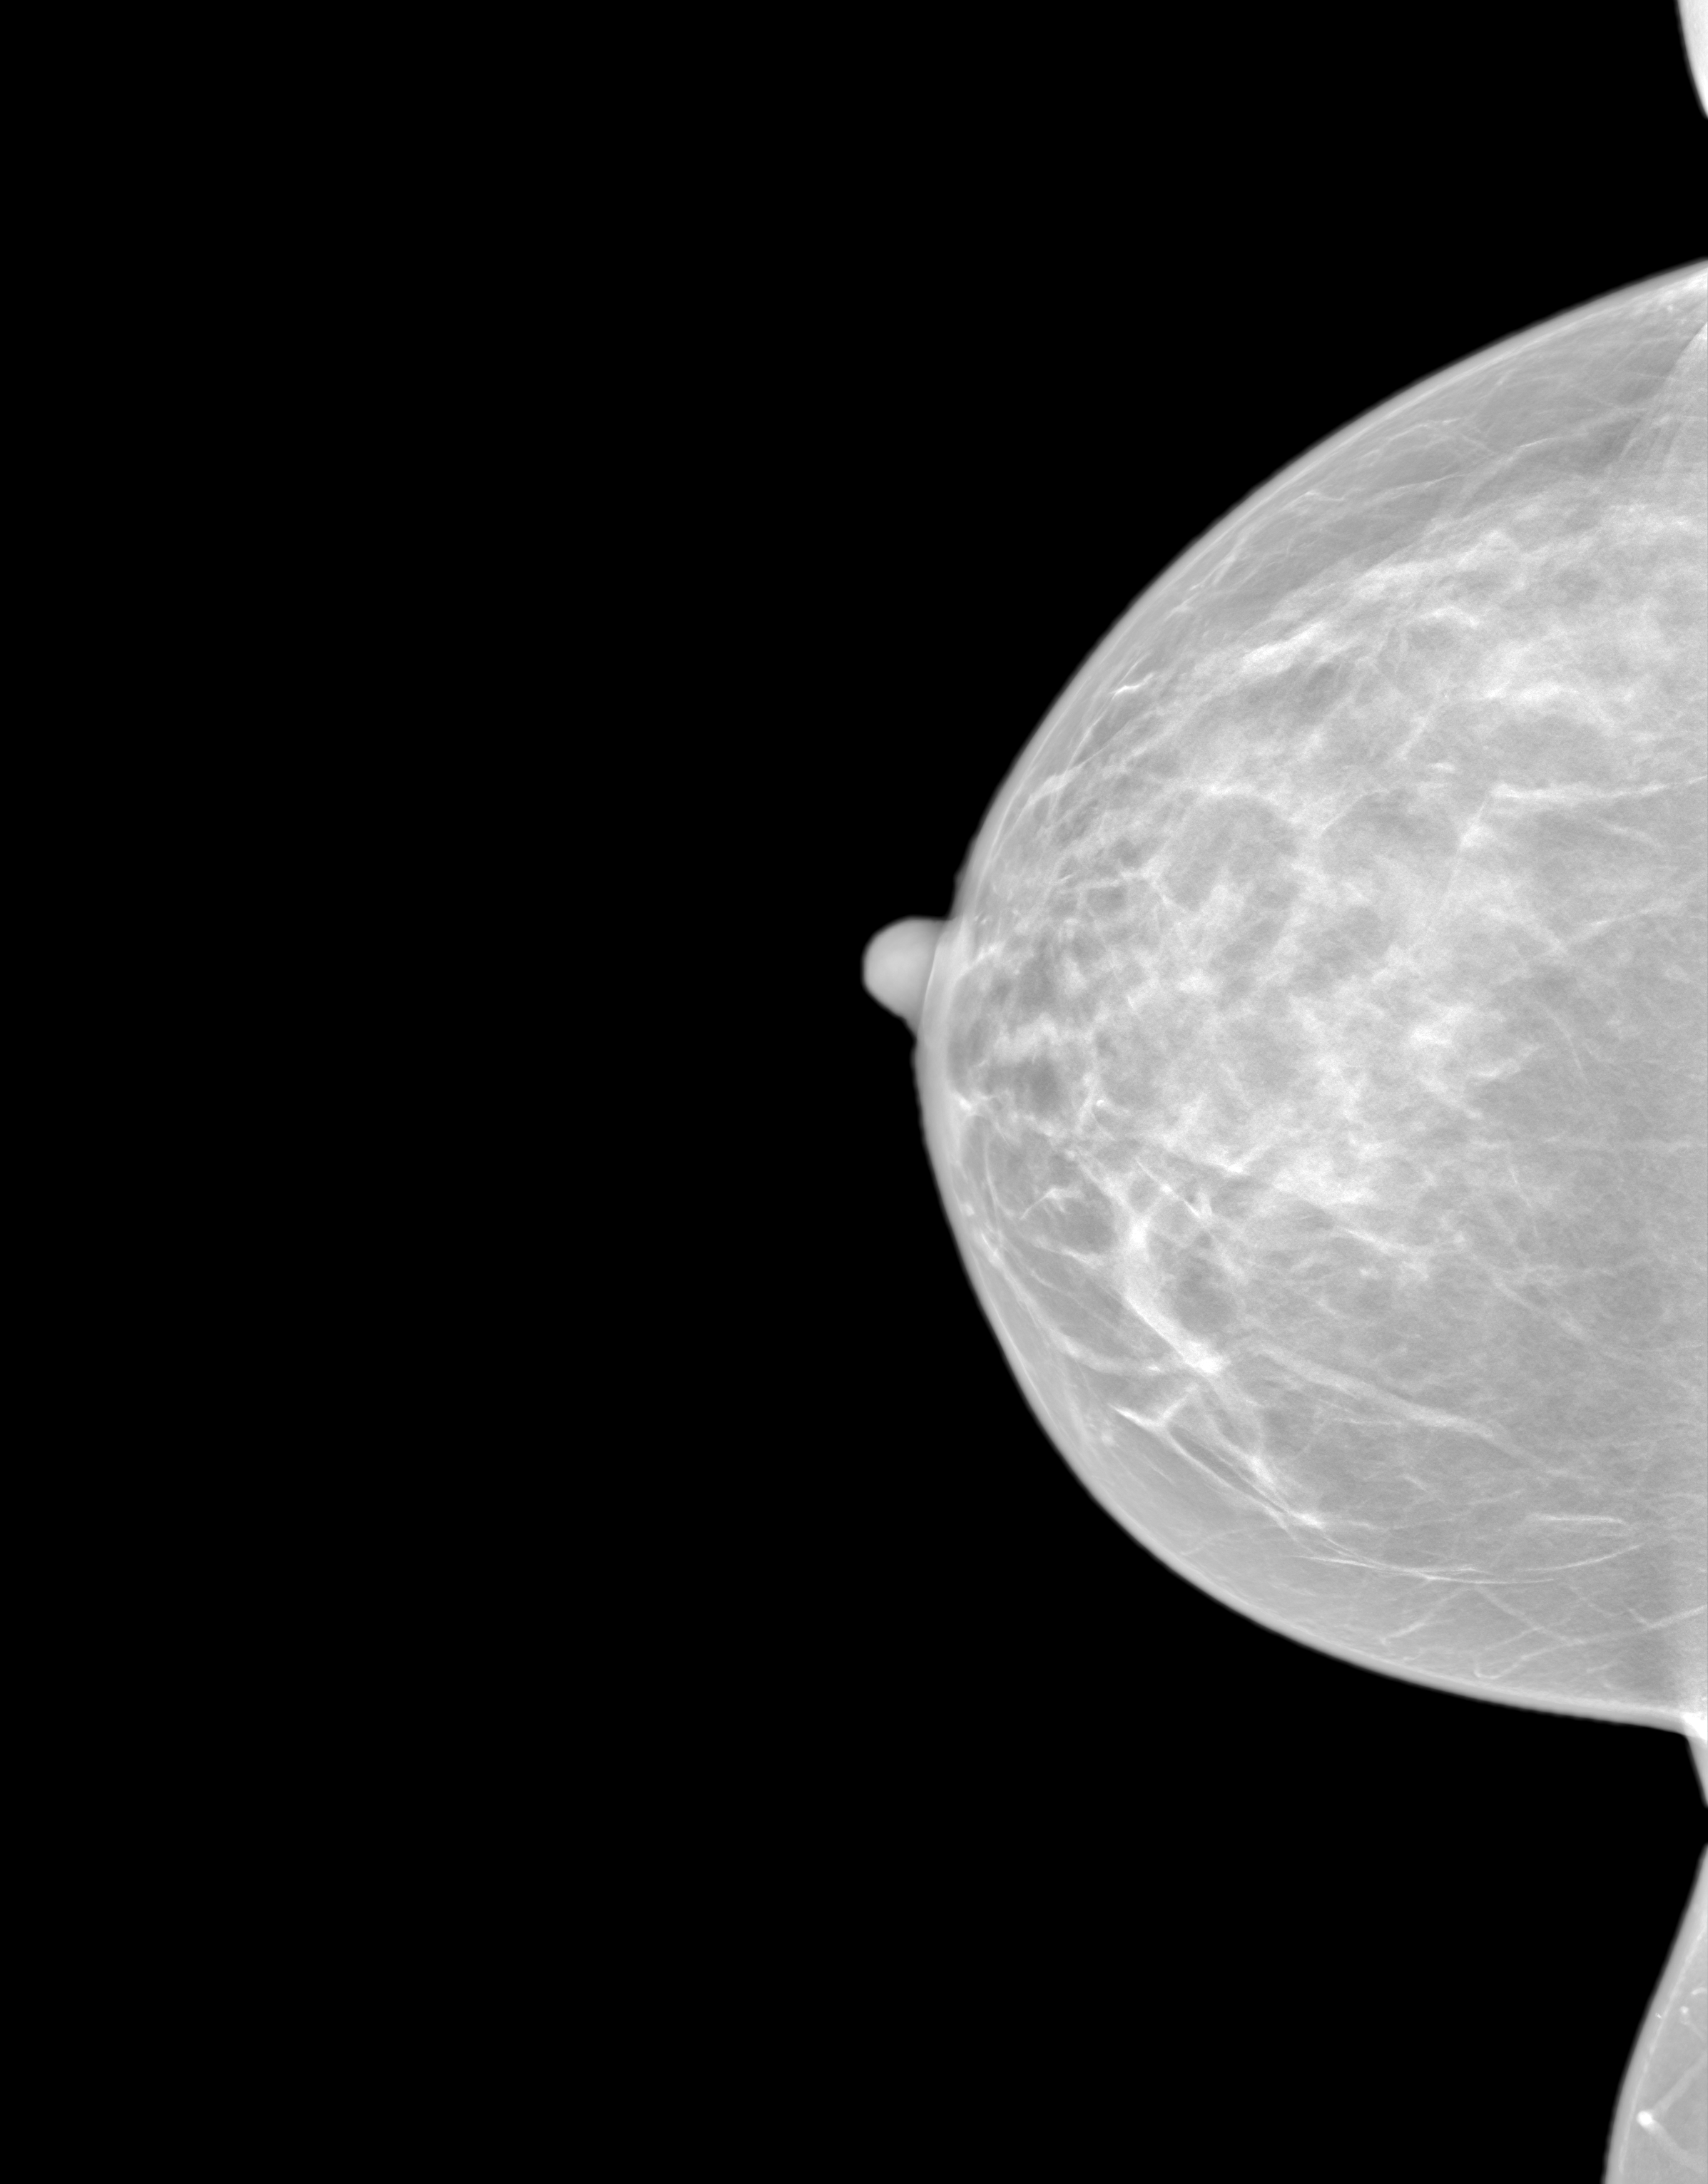
Screening examination. Patient aged 49 years (female).
Image type: synthesized 2-D view from tomosynthesis. Breast: right. Projection: craniocaudal (CC) view. Breast density at the screening exam (both breasts): heterogeneously dense (BI-RADS density category c). Final BI-RADS assessment for this screening round (tomosynthesis exam, both breasts): category 1. Recall: no recall after this screen.